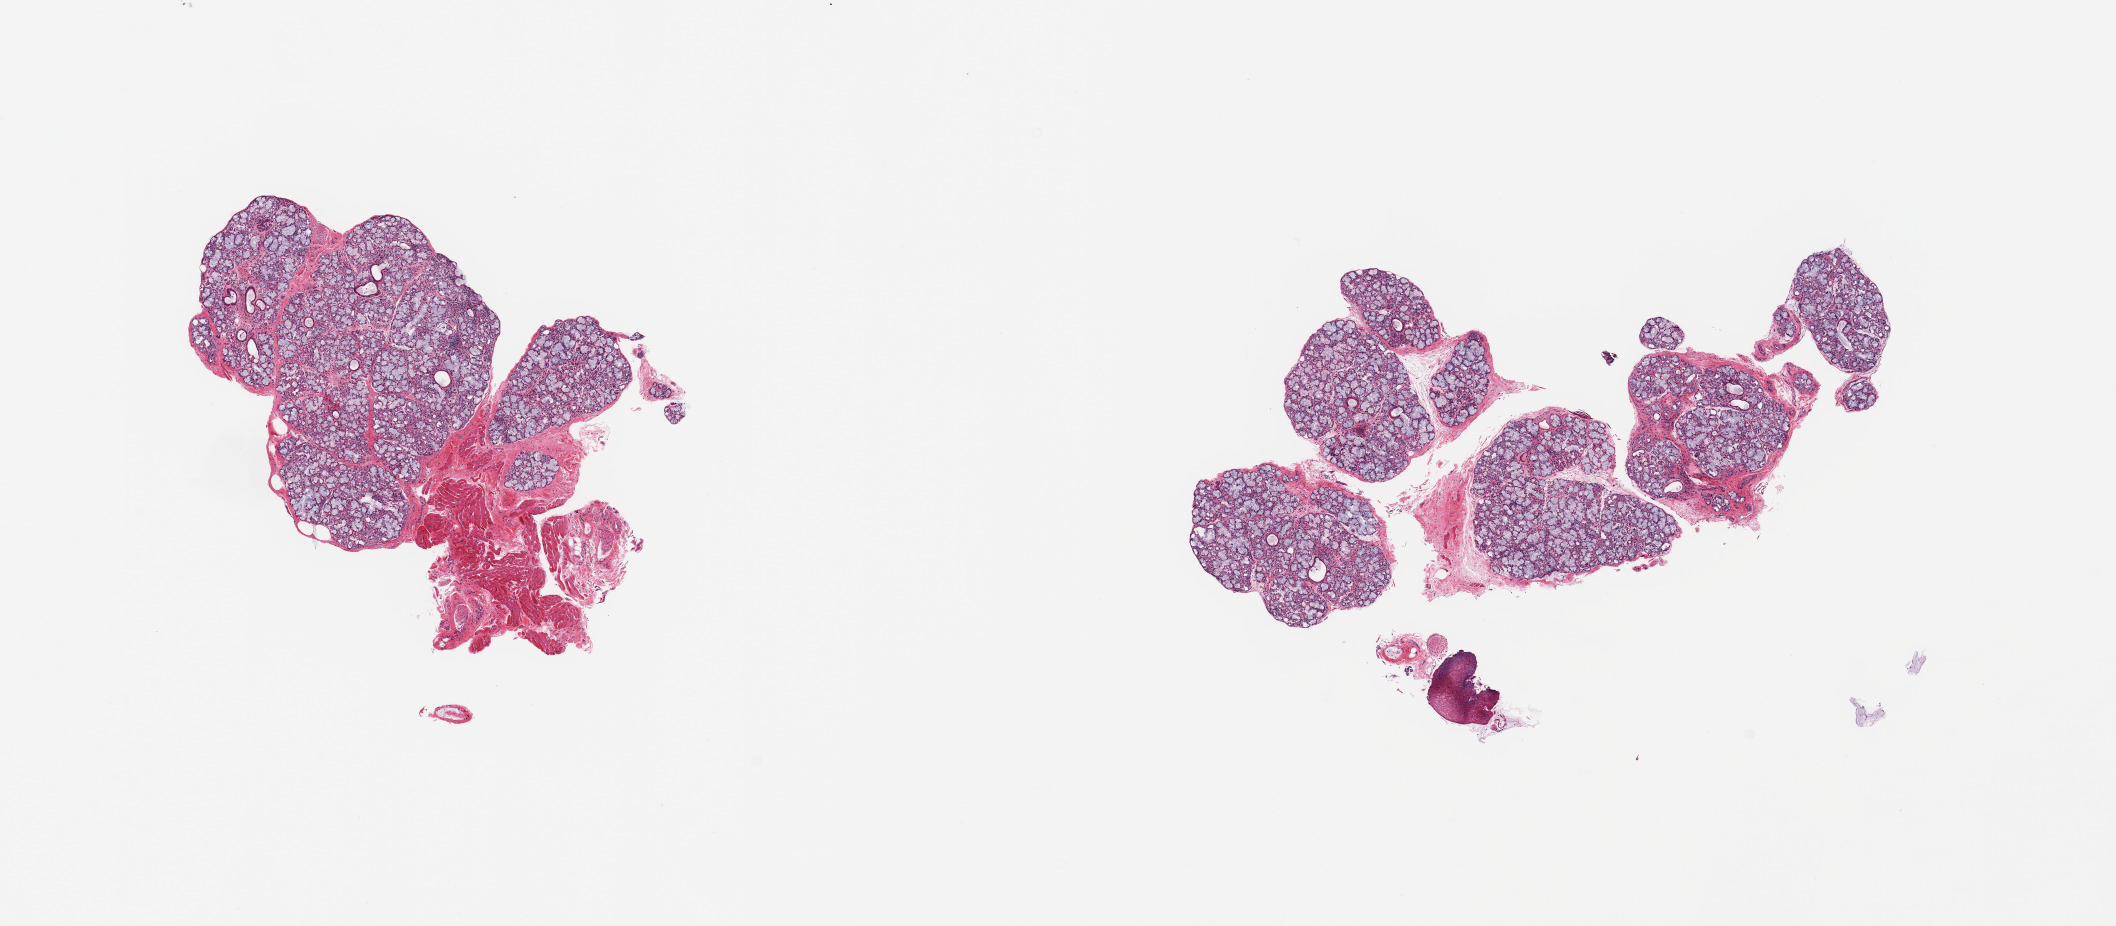
H&E whole-slide image — shown as a low-resolution overview of the whole scanned area (about 16.7 x 7.3 mm), PAXgene-fixed paraffin-embedded (PFPE) section, target tissue: minor salivary gland, donor tissue sample. Donor sex: female.
* pathologist's review note for this sample: 2 pieces, ~95% glandular/ductal elements, good specimen